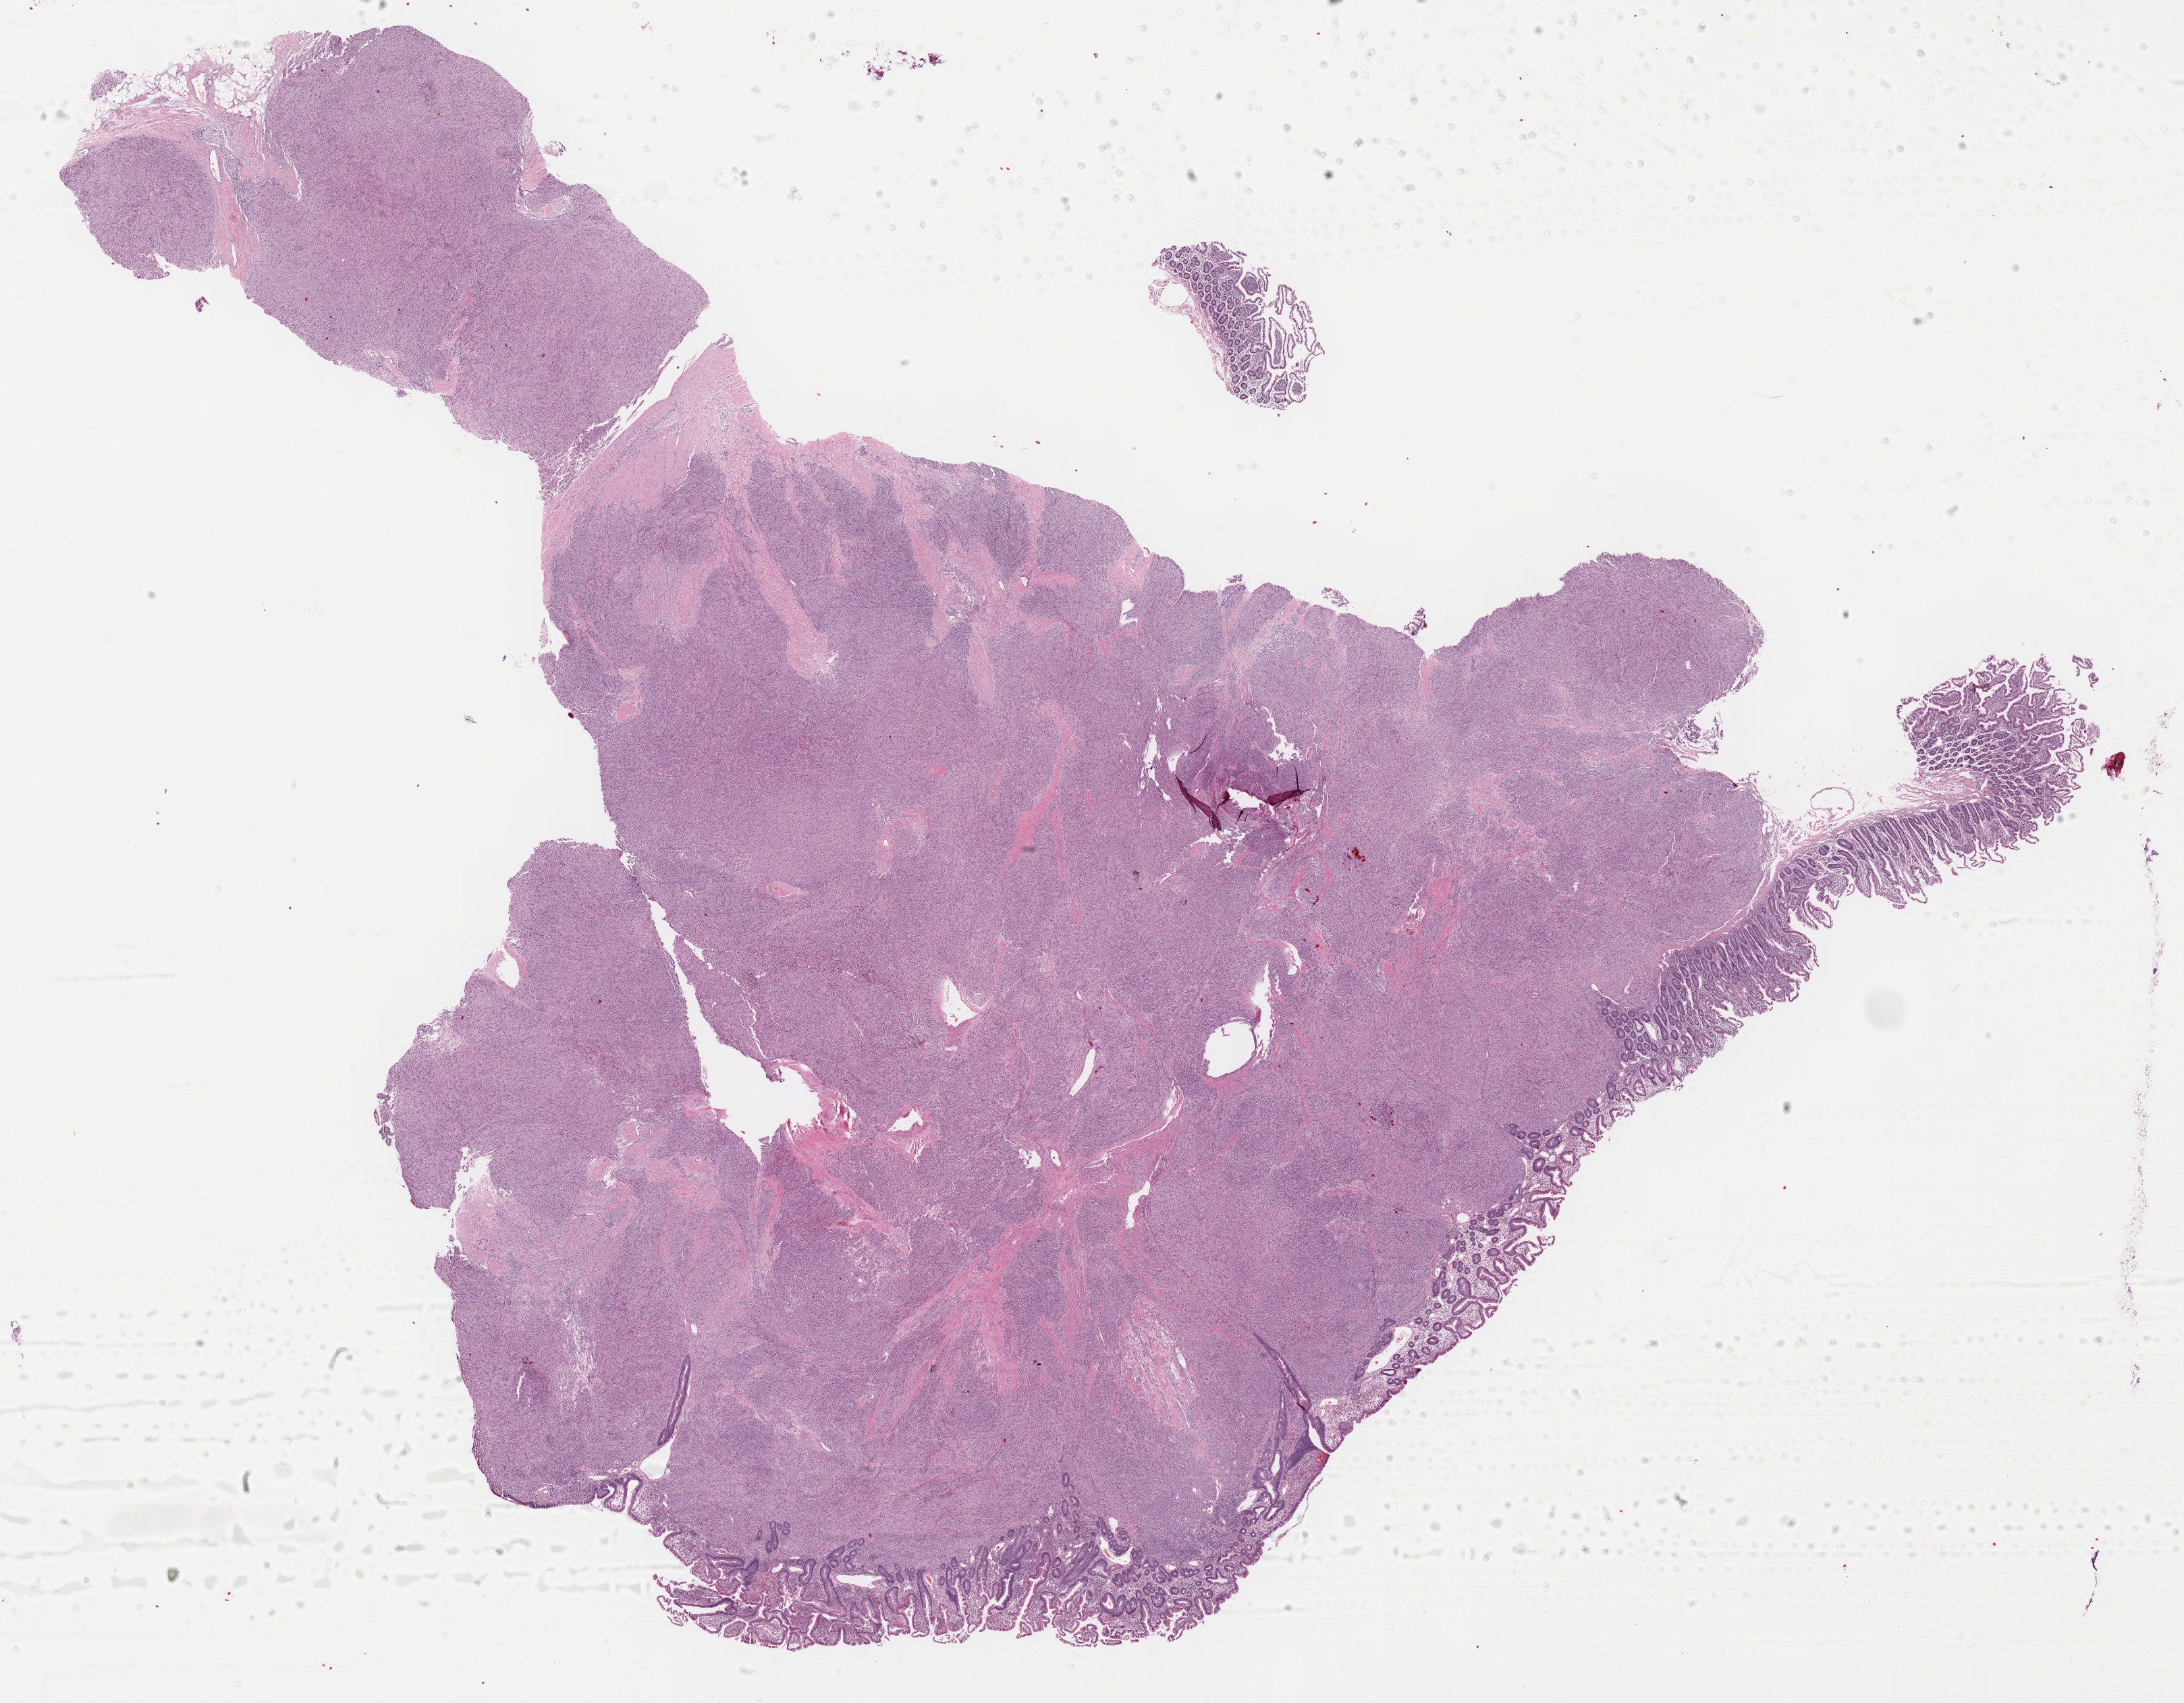
Hematoxylin and eosin (H&E) stained whole-slide image — a low-resolution overview of the entire scanned area, about 26.2 x 20.4 mm (acquisition: 40x scan), FFPE section, primary tumour sample from the retroperitoneum and peritoneum. Male patient; age at initial diagnosis 54 years.
• pathologic diagnosis: Leiomyosarcoma, NOS (retroperitoneum)